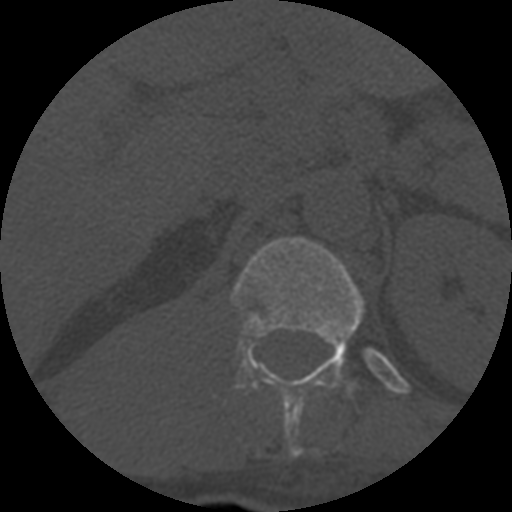
CT including the spine, one axial slice; position 312 of 708 along the scan axis; reconstruction kernel STANDARD; one of 3 acquisitions stored at this slice position; bone window (W 1800 / L 400 HU); 1.25 mm slice thickness; 512 × 512 image matrix. Patient age 55 years. From the clinical record (not read from this slice): primary cancer: colon.
Annotated regions visible in this slice (semi-automatic segmentation, software-assisted and operator-edited):
- T12 vertebra: bounding box <231,237,364,457> (left, top, right, bottom; pixels)